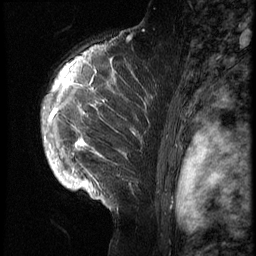
Breast MRI (dynamic contrast-enhanced), one sagittal slice. Slice 47 of 70 in the series (ordered by position). 3 images stored at this slice position (order not interpretable as contrast timing). 1.5 T. TE 4.2 ms, TR 9 ms. 2.5 mm slice thickness. 256 × 256 image matrix. Female patient, age 28 years. Case-level facts recorded for this patient, not image findings: setting: breast cancer imaged before/during neoadjuvant chemotherapy.
Outlined on this slice (semi-automatic segmentation, software-assisted and operator-edited):
- analysis volume of interest (the breast-tissue region the enhancement analysis was run in; not a lesion): box from (x=43, y=42) to (x=157, y=215) px
- tumour enhancement mask (voxels above the 140 % enhancement threshold inside the analysis volume of interest): (x=50, y=47)–(x=114, y=192)